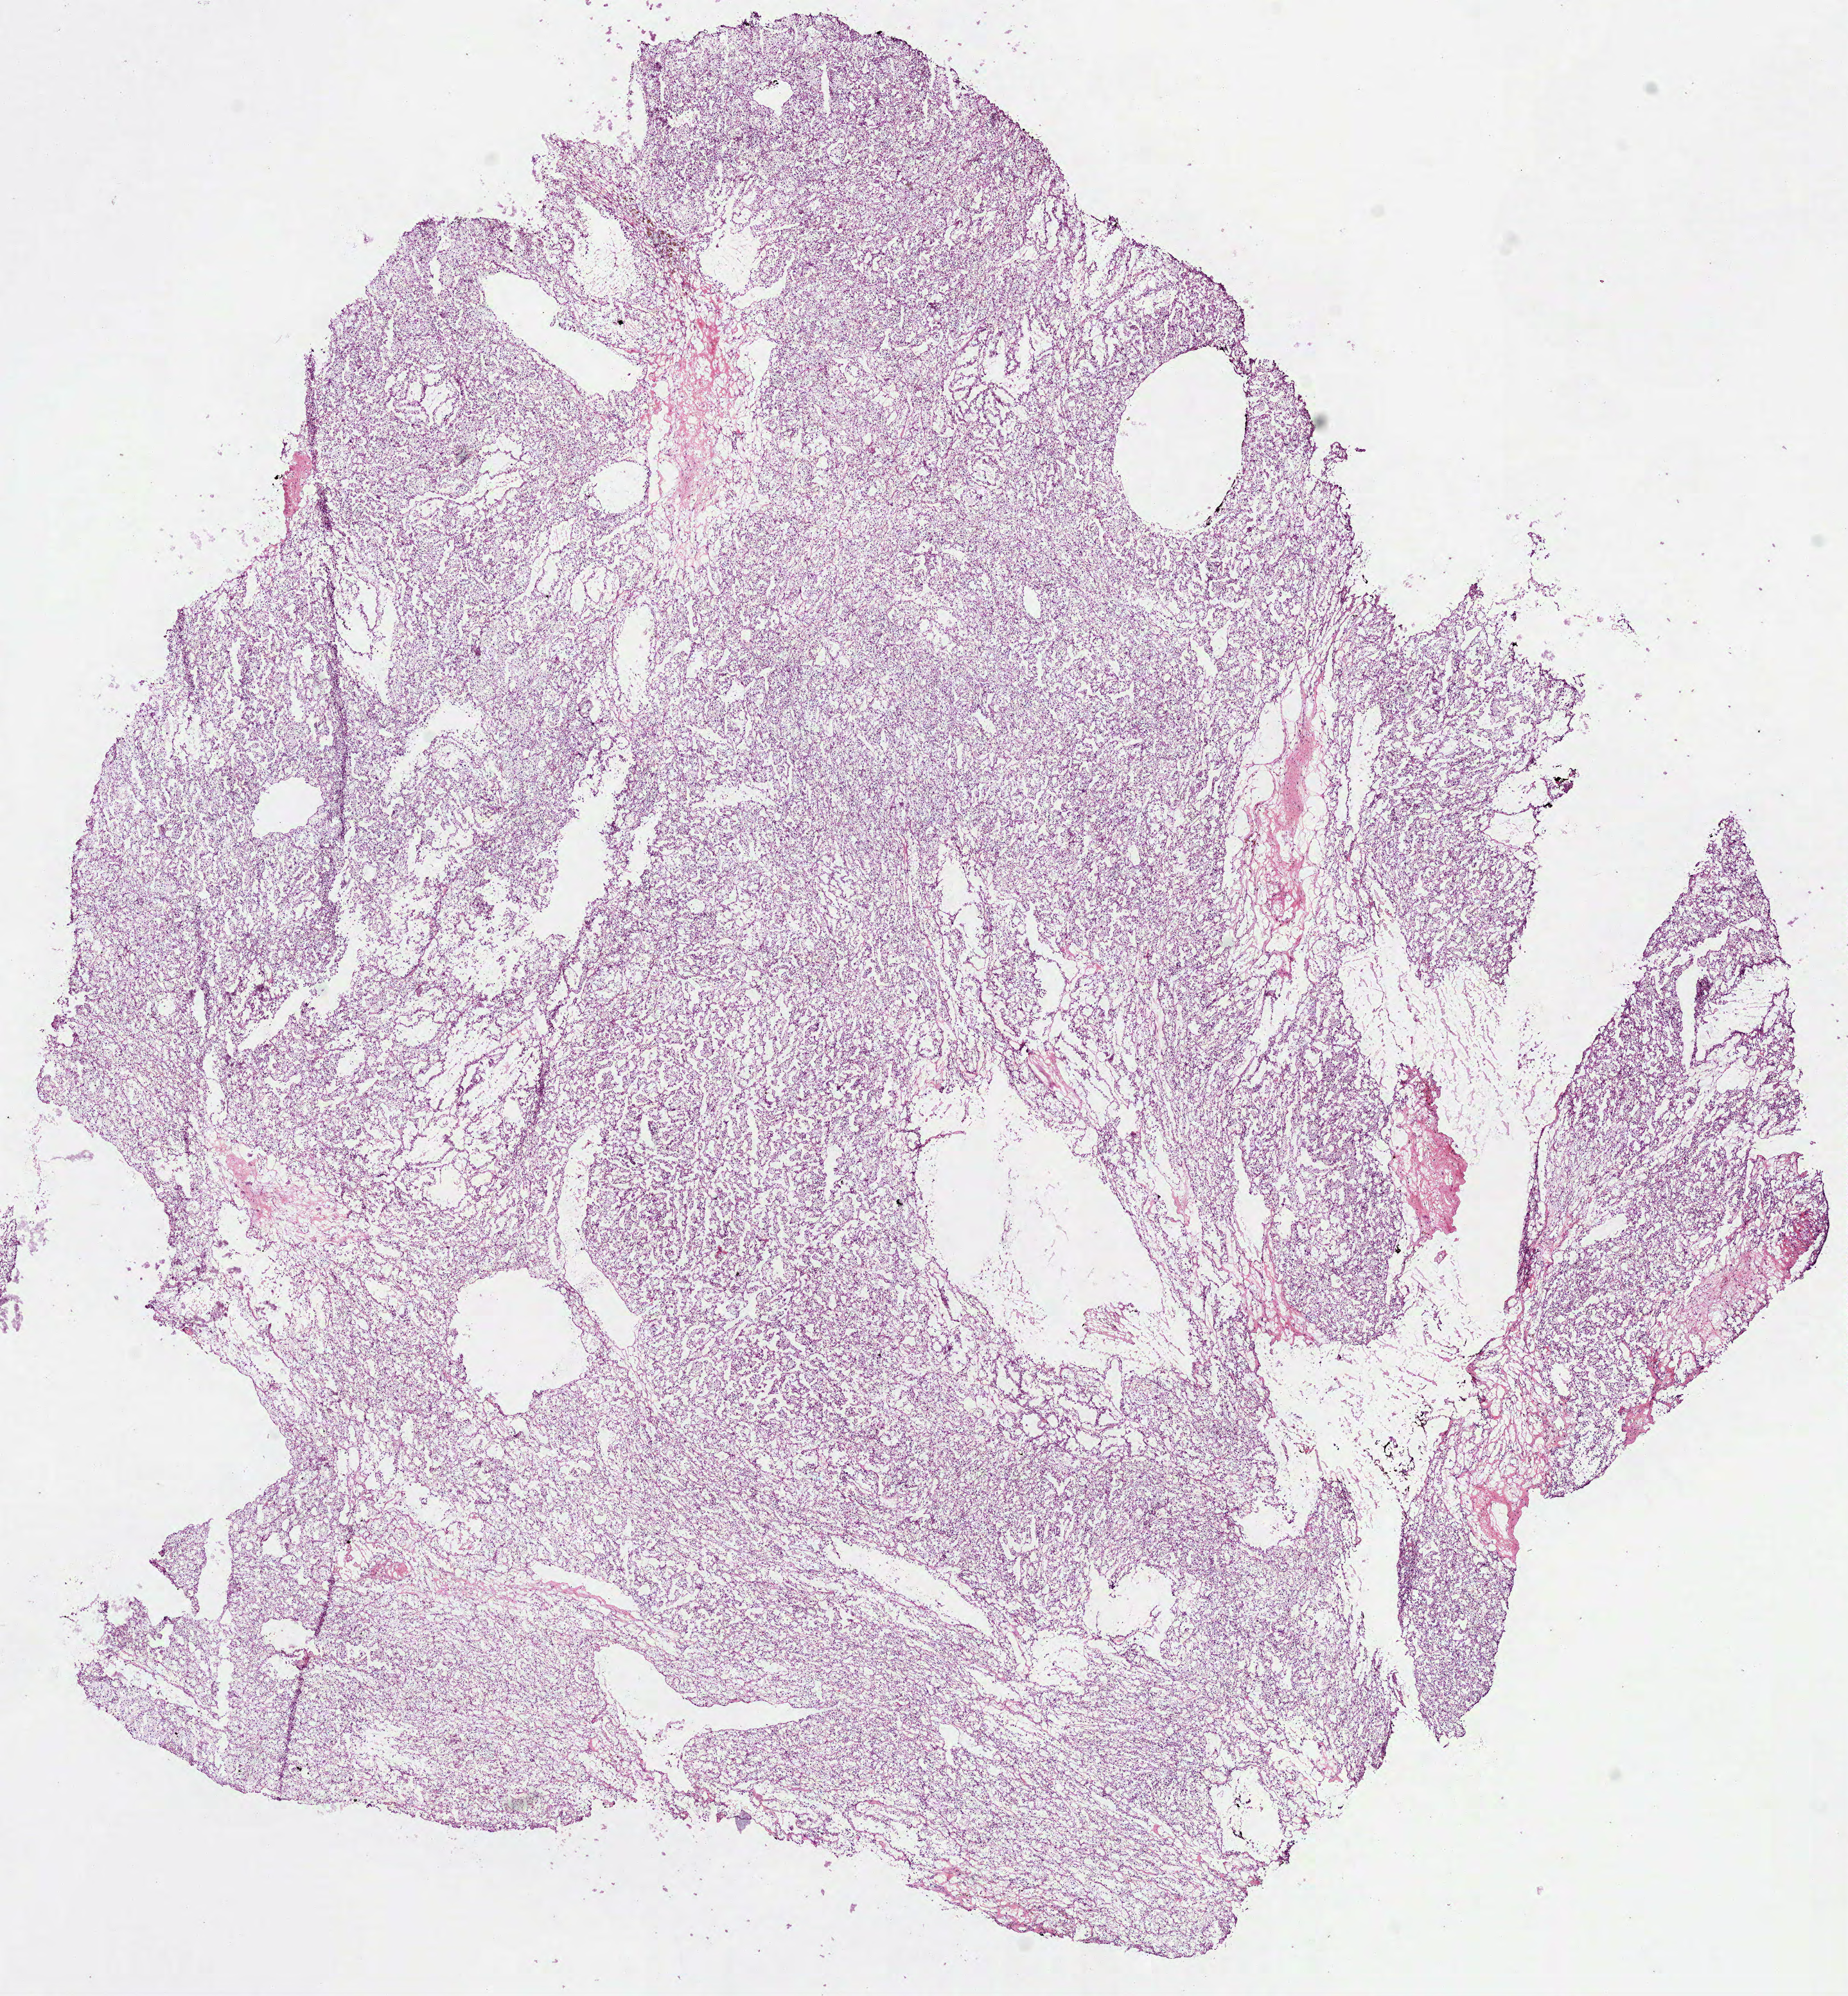
Whole-slide histology image, H&E, shown as a low-resolution overview of the whole scanned area (about 11.6 x 12.5 mm); frozen section from the bottom of the tissue portion; sample: primary tumour, kidney. Male, age 61 years at initial diagnosis. Histologic grade: G3 (poorly differentiated). Slide review estimates, as recorded: tumour cells 95%, tumour nuclei 85%, normal cells 0%, stromal cells 5%, necrosis 0%.
AJCC pathologic stage: I. Pathologic diagnosis: Clear cell adenocarcinoma, NOS.